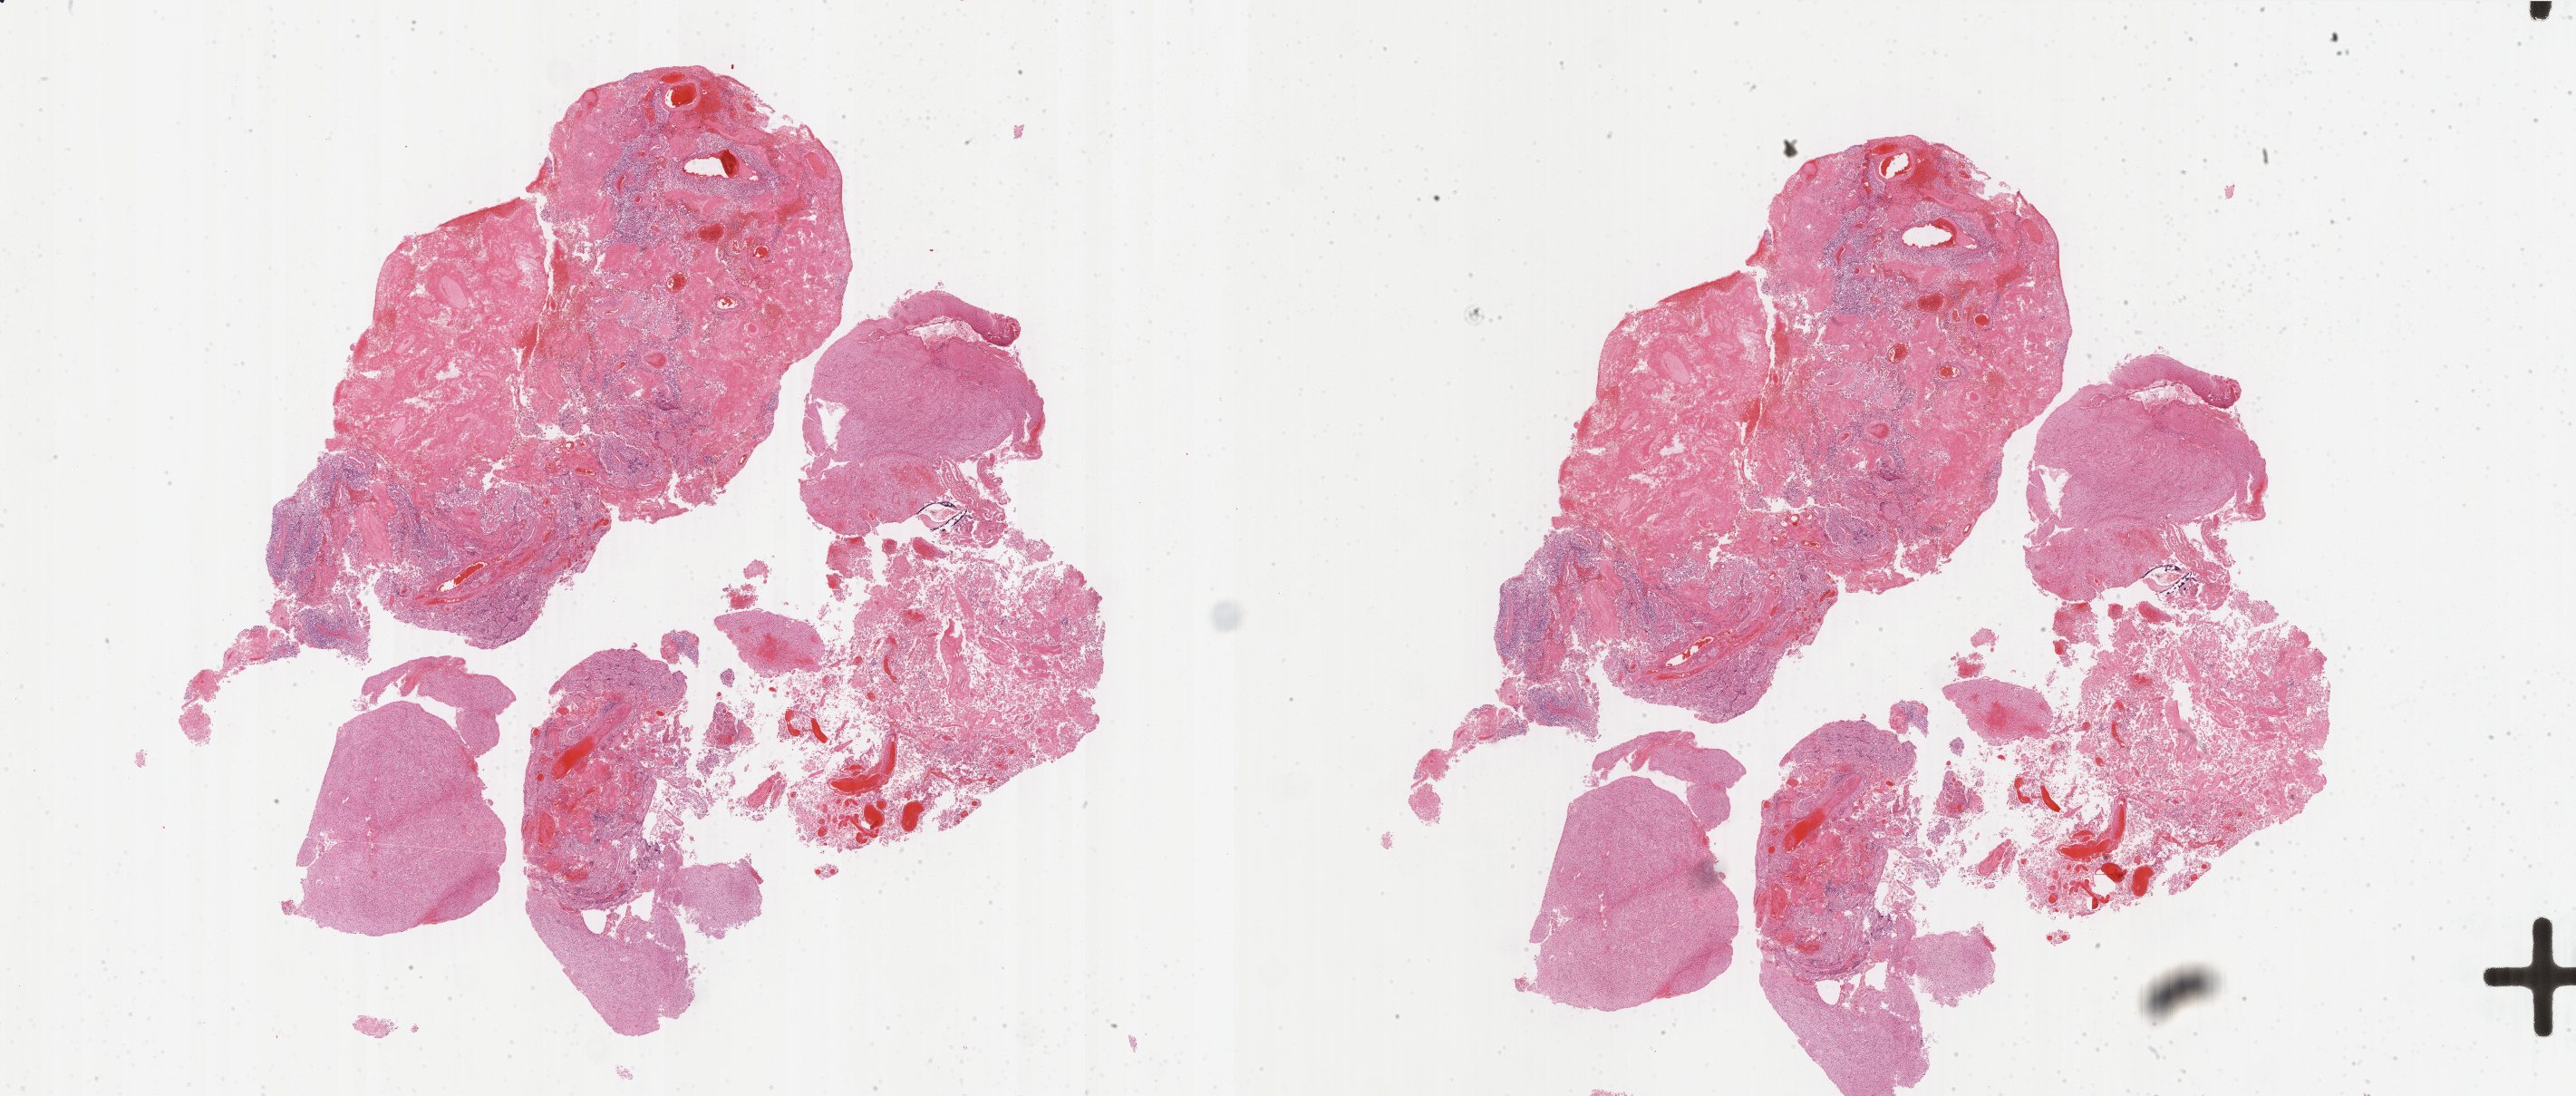
Whole-slide histology image, H&E, whole scanned area (about 45.2 x 19.2 mm) shown as a low-resolution overview. Formalin-fixed paraffin-embedded (FFPE) diagnostic section. Sample: primary tumour, brain. Male, age 43 years at initial diagnosis.
Pathologic diagnosis: Glioblastoma.